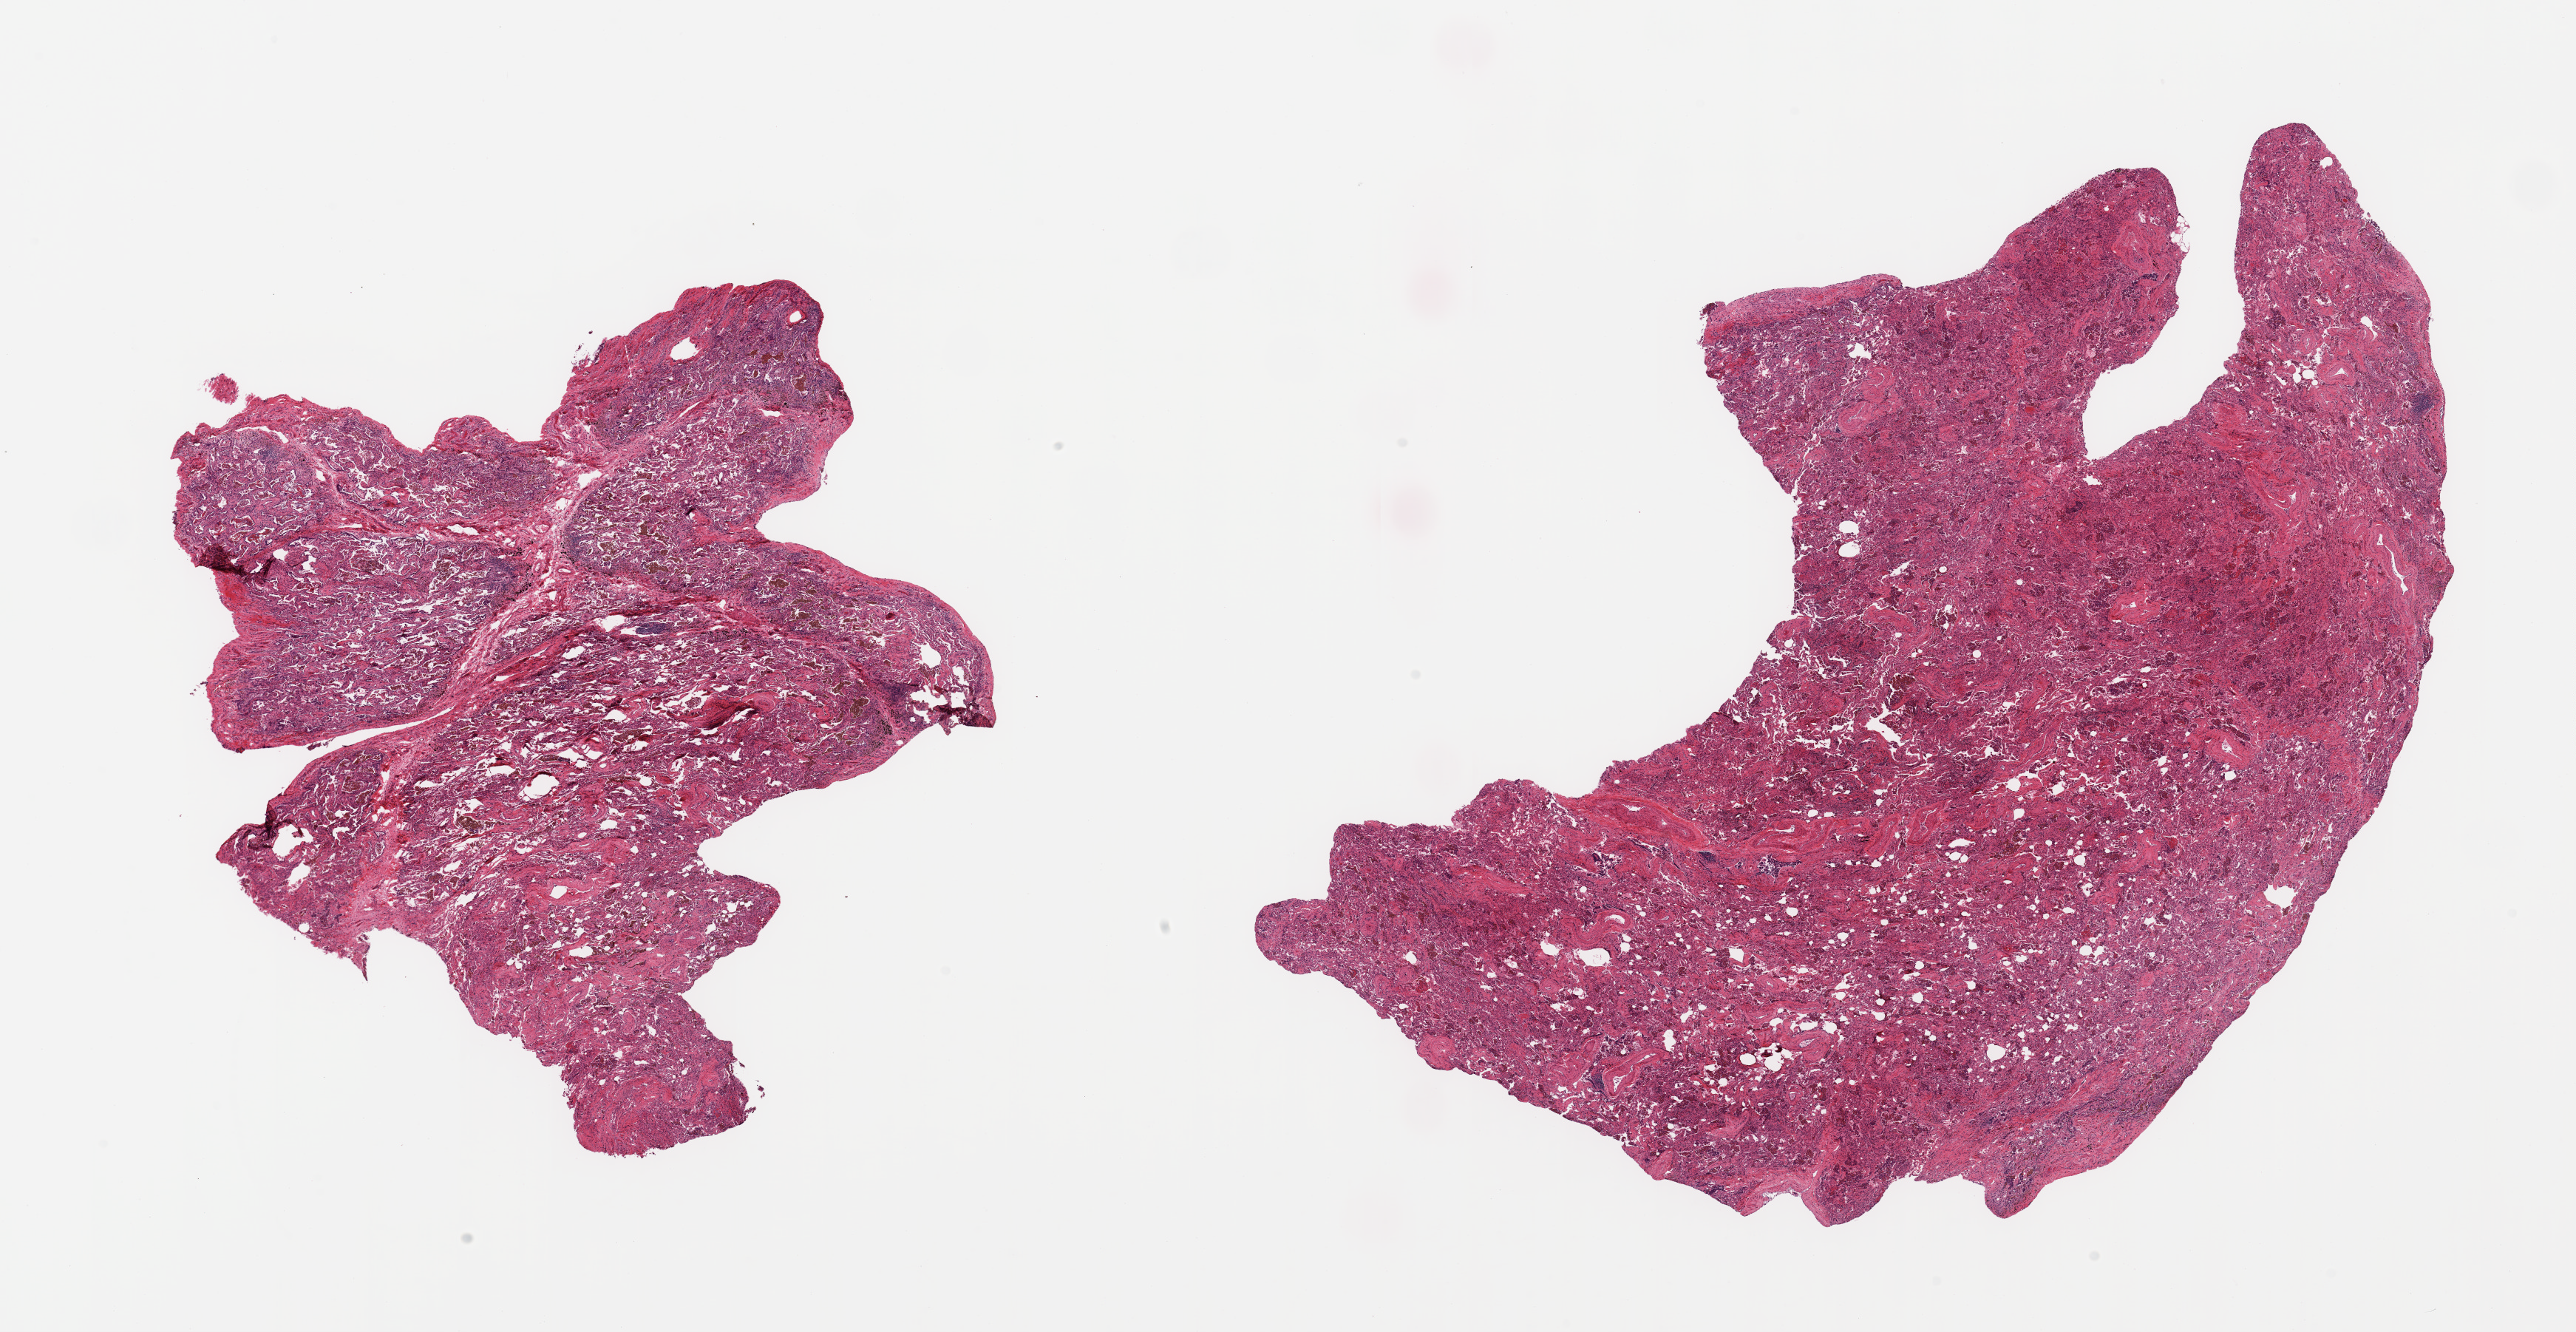
Digitized haematoxylin and eosin-stained section, brightfield — whole scanned area (about 27.6 x 14.3 mm, slide scanned at 20x) shown as a low-resolution overview, PAXgene-fixed paraffin-embedded (PFPE) section, target tissue: lung, tissue donor sample. Male donor.
Pathologist's review note for this sample: 2 pieces; severe interstitial and vascular fibrosis with numerous pigmented alveolar macrophages (heart failure cells).